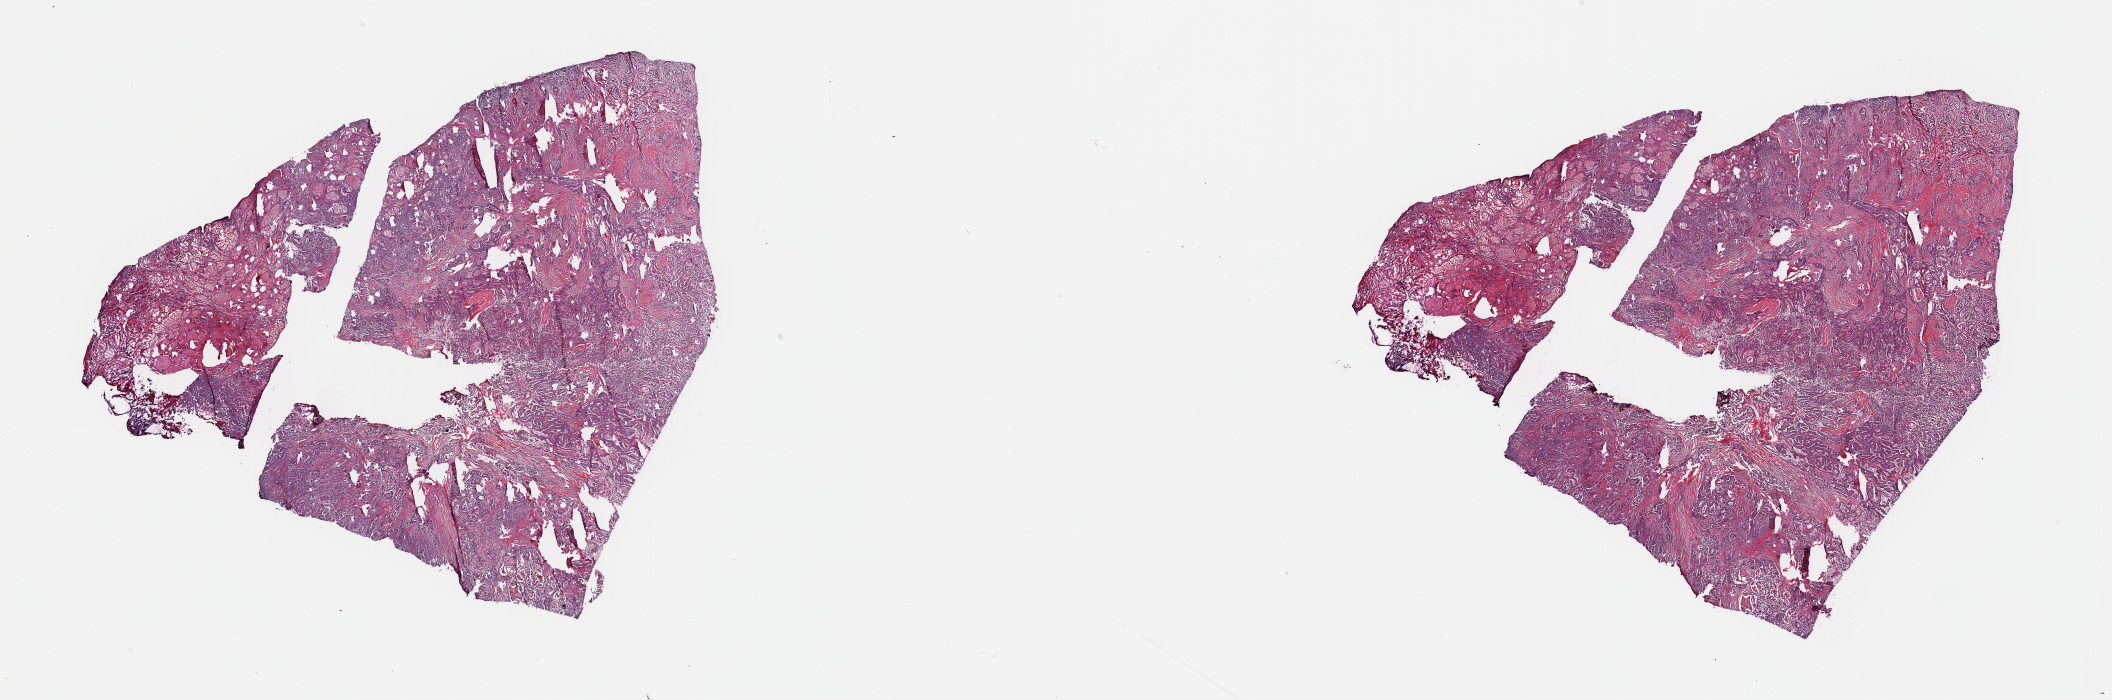
Whole-slide histology image, Hematoxylin and eosin (H&E) stained — low-resolution overview of the scanned area, about 33.4 x 11.1 mm (from a 40x scan), frozen section from the top of the tissue portion, primary tumour sample from the thyroid. Male, age 39 years at initial diagnosis. Slide review estimates, as recorded: tumour cells 90%, tumour nuclei 82%, normal cells 0%, stromal cells 10%, necrosis 0%. Infiltration values recorded for this section: lymphocyte infiltration 0%, monocyte infiltration 0%, neutrophil infiltration 0%.
• AJCC pathologic stage: I (6th edition)
• diagnosis: Papillary carcinoma, columnar cell (thyroid gland)
• laterality: midline
• lymph nodes positive (case pathology): 0 of 4 examined